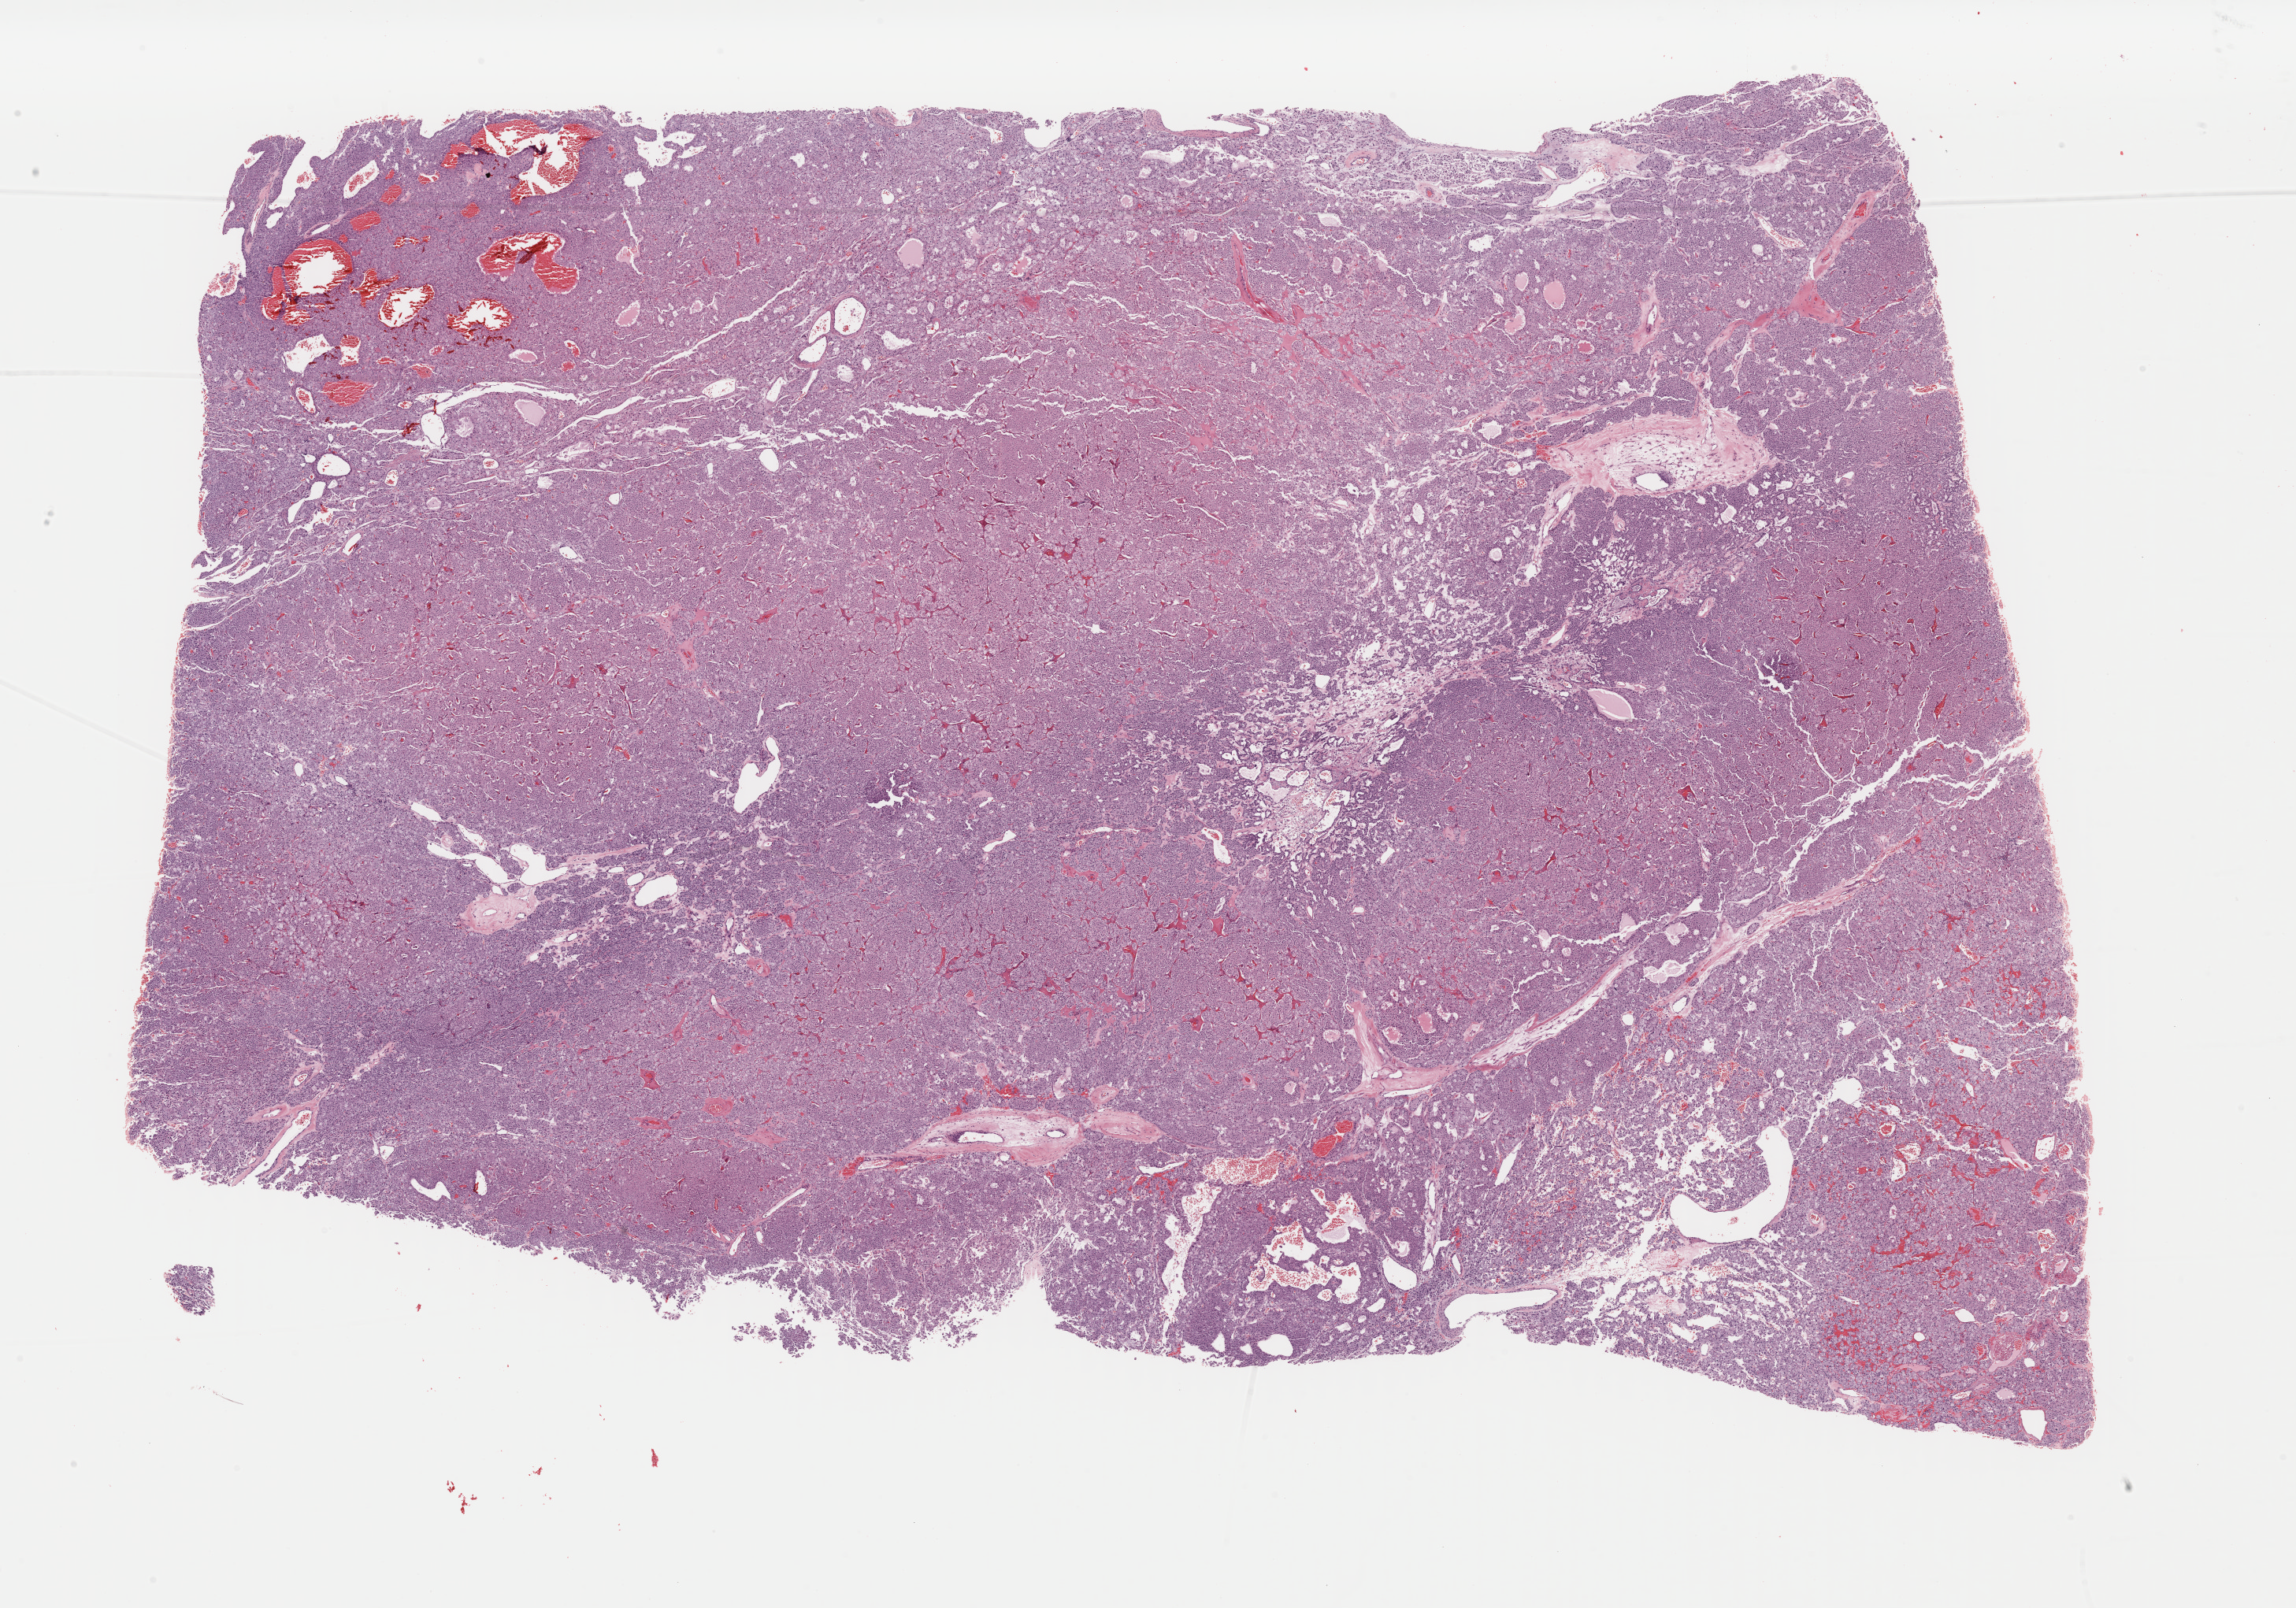
Whole-slide histology image, H&E, shown as a low-resolution overview of the whole scanned area (about 23.0 x 16.1 mm), formalin-fixed paraffin-embedded (FFPE) diagnostic section, sample: primary tumour, kidney. Patient: male, age at initial diagnosis 69 years.
* pathologic diagnosis: Renal cell carcinoma, chromophobe type
* AJCC pathologic stage: II